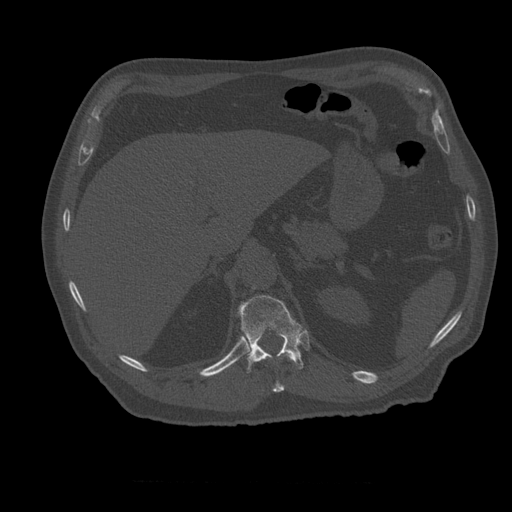
CT including the spine, one axial slice. Reconstruction kernel STANDARD. 120 kVp. Bone window (W 1800 / L 400 HU). 512 × 512 image matrix, field of view 407 × 407 mm. Patient age 73 years. From the clinical record (not read from this slice): primary cancer: prostate; vertebrae with lytic lesions (as recorded): L2.
Structures marked on this image (semi-automatic segmentation, software-assisted and operator-edited):
- T11 vertebra: bounding box <262,359,285,393> (left, top, right, bottom; pixels)
- T12 vertebra: <238,295,304,373>